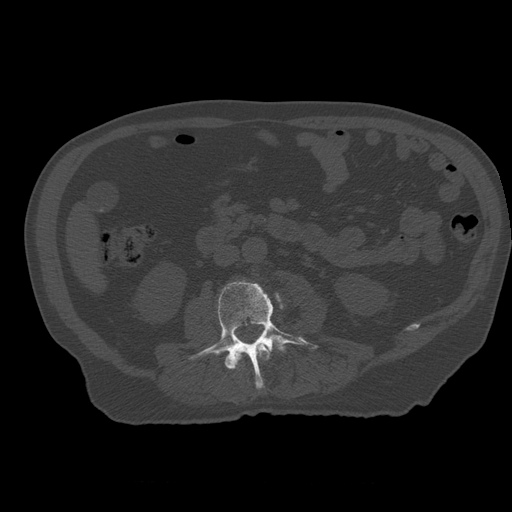
CT including the spine, one axial slice. Position 191 of 399 along the scan axis. 120 kVp. Bone window (W 1800 / L 400 HU). 1.25 mm slice thickness. 512 × 512 image matrix. Patient age 73 years. From the clinical record (not read from this slice): primary cancer: prostate; vertebrae with lytic lesions (as recorded): L2.
Annotated regions visible in this slice (semi-automatic segmentation, software-assisted and operator-edited):
- L2 vertebra: bounding box <232,343,271,369> (left, top, right, bottom; pixels)
- L3 vertebra: <189,281,318,389>